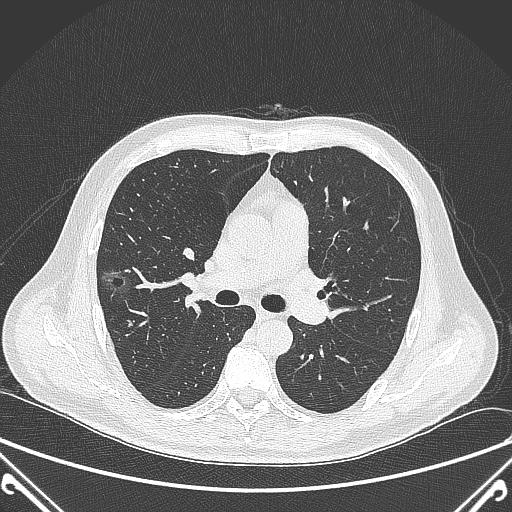
Chest CT, one axial slice; position 224 of 360 along the scan axis; lung window (W 1500 / L -600 HU); 512 × 512 image matrix, field of view 380 × 380 mm. Patient: male, 64 years. Case-level facts recorded for this patient, not image findings: clinical TNM (as recorded): T1c N0 M0; histopathological grade: G2.
Outlined on this slice (rectangle marked by the reading radiologist):
- lung tumour (recorded histology: adenocarcinoma): bounding box [x1, y1, x2, y2] px = [95, 262, 137, 305]